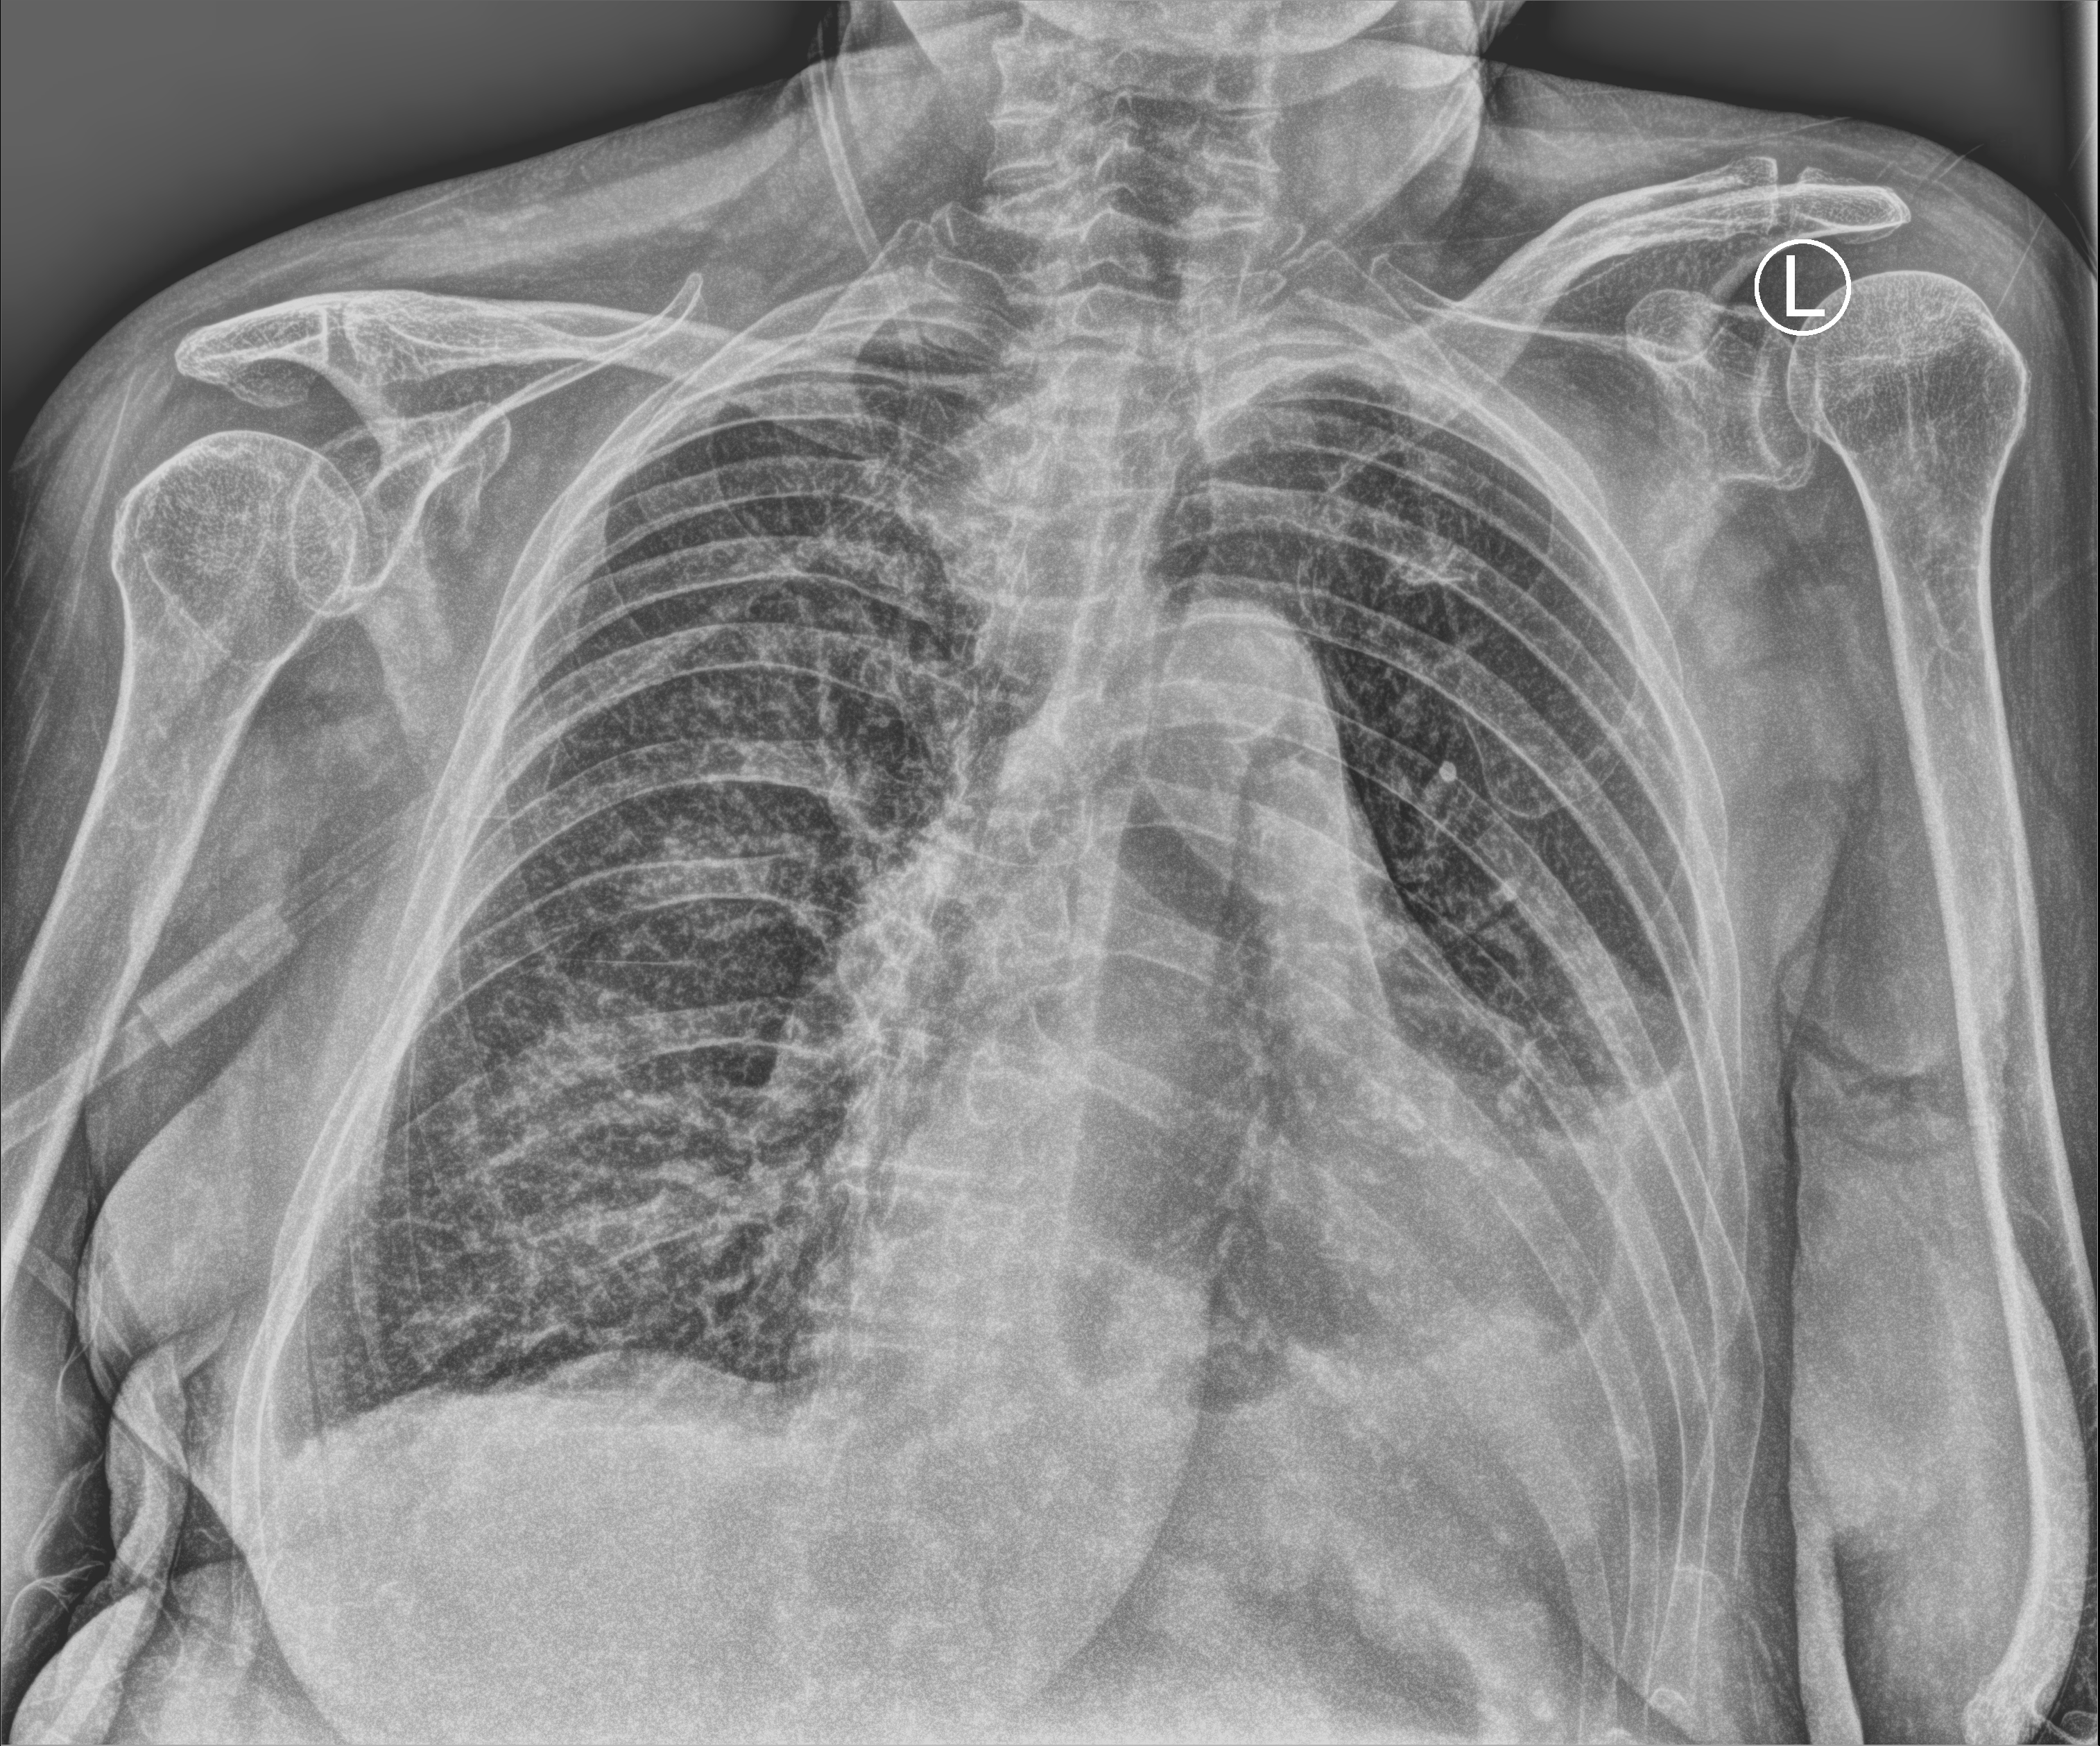
Portable chest radiograph, anteroposterior (AP) projection. Female patient hospitalised with COVID-19, age 75–90 years.
Hospital-stay facts (about this admission, not read from this image; timing relative to this image not recorded): admitted to intensive care during this hospital stay: no.